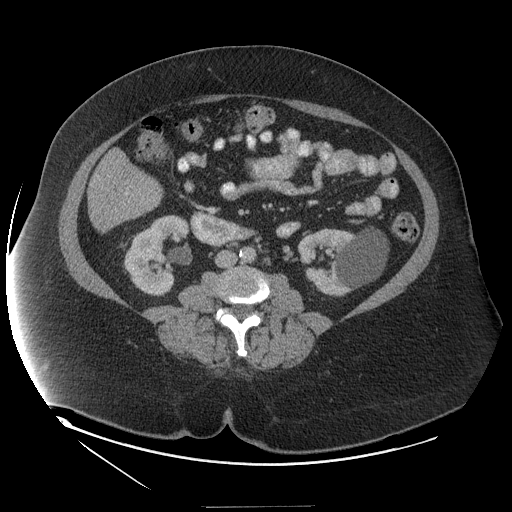
Contrast-enhanced abdominal CT (liver protocol), one axial slice; slice 31 of 127 in the series (ordered by position); reconstruction kernel STANDARD; soft-tissue window (W 400 / L 40 HU); 512 × 512 image matrix. Case-level facts recorded for this patient, not image findings: diagnosis: hepatocellular carcinoma (patient treated with transarterial chemoembolisation; whether this scan precedes or follows treatment is not stated here); TNM stage (as recorded): Stage-II; Child-Pugh class: A; tumour differentiation: well differentiated; tumour size: 3 cm.
Structures marked on this image (semi-automatic segmentation, software-assisted and operator-edited):
- liver parenchyma outside the tumour (the mass and vessels are separate outlines, so this box may not span the whole liver): bounding box <88,194,151,231> (left, top, right, bottom; pixels)